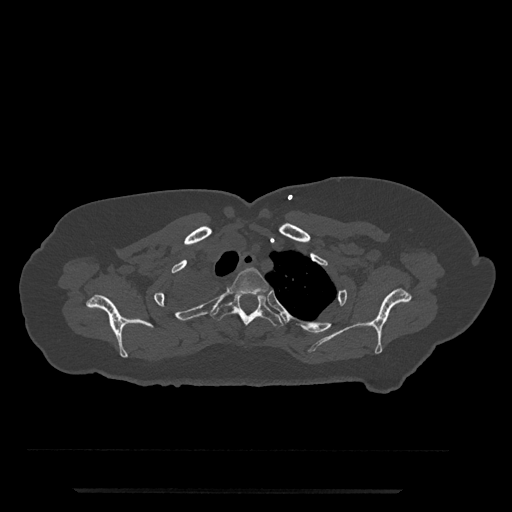
CT including the spine, one axial slice. Reconstruction kernel Br40s/3. Bone window (W 1800 / L 400 HU). 0.5 mm slice thickness. 512 × 512 image matrix, field of view 440 × 440 mm. Female patient, age 51 years. From the clinical record (not read from this slice): primary cancer: neuro; vertebrae with lytic lesions (as recorded): T8.
Annotated regions visible in this slice (semi-automatically segmented with operator editing):
- T2 vertebra: bounding box <228,267,269,295> (left, top, right, bottom; pixels)
- T3 vertebra: <211,293,284,327>